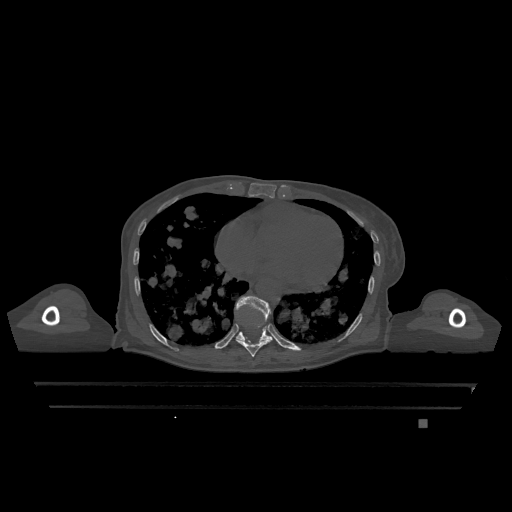
CT including the spine, one axial slice. Position 672 of 1317 along the scan axis. Bone window (W 1800 / L 400 HU). 0.5 mm slice thickness. 512 × 512 image matrix. Female patient, age 74 years. From the clinical record (not read from this slice): primary cancer: lung; vertebrae with lytic lesions (as recorded): T1, T4, T5, T6, L4, L5.
Annotated regions visible in this slice (semi-automatically segmented with operator editing):
- T10 vertebra: bounding box (x1, y1, x2, y2) in pixels: (235, 296, 272, 341)
- T9 vertebra: (236, 325, 272, 357)